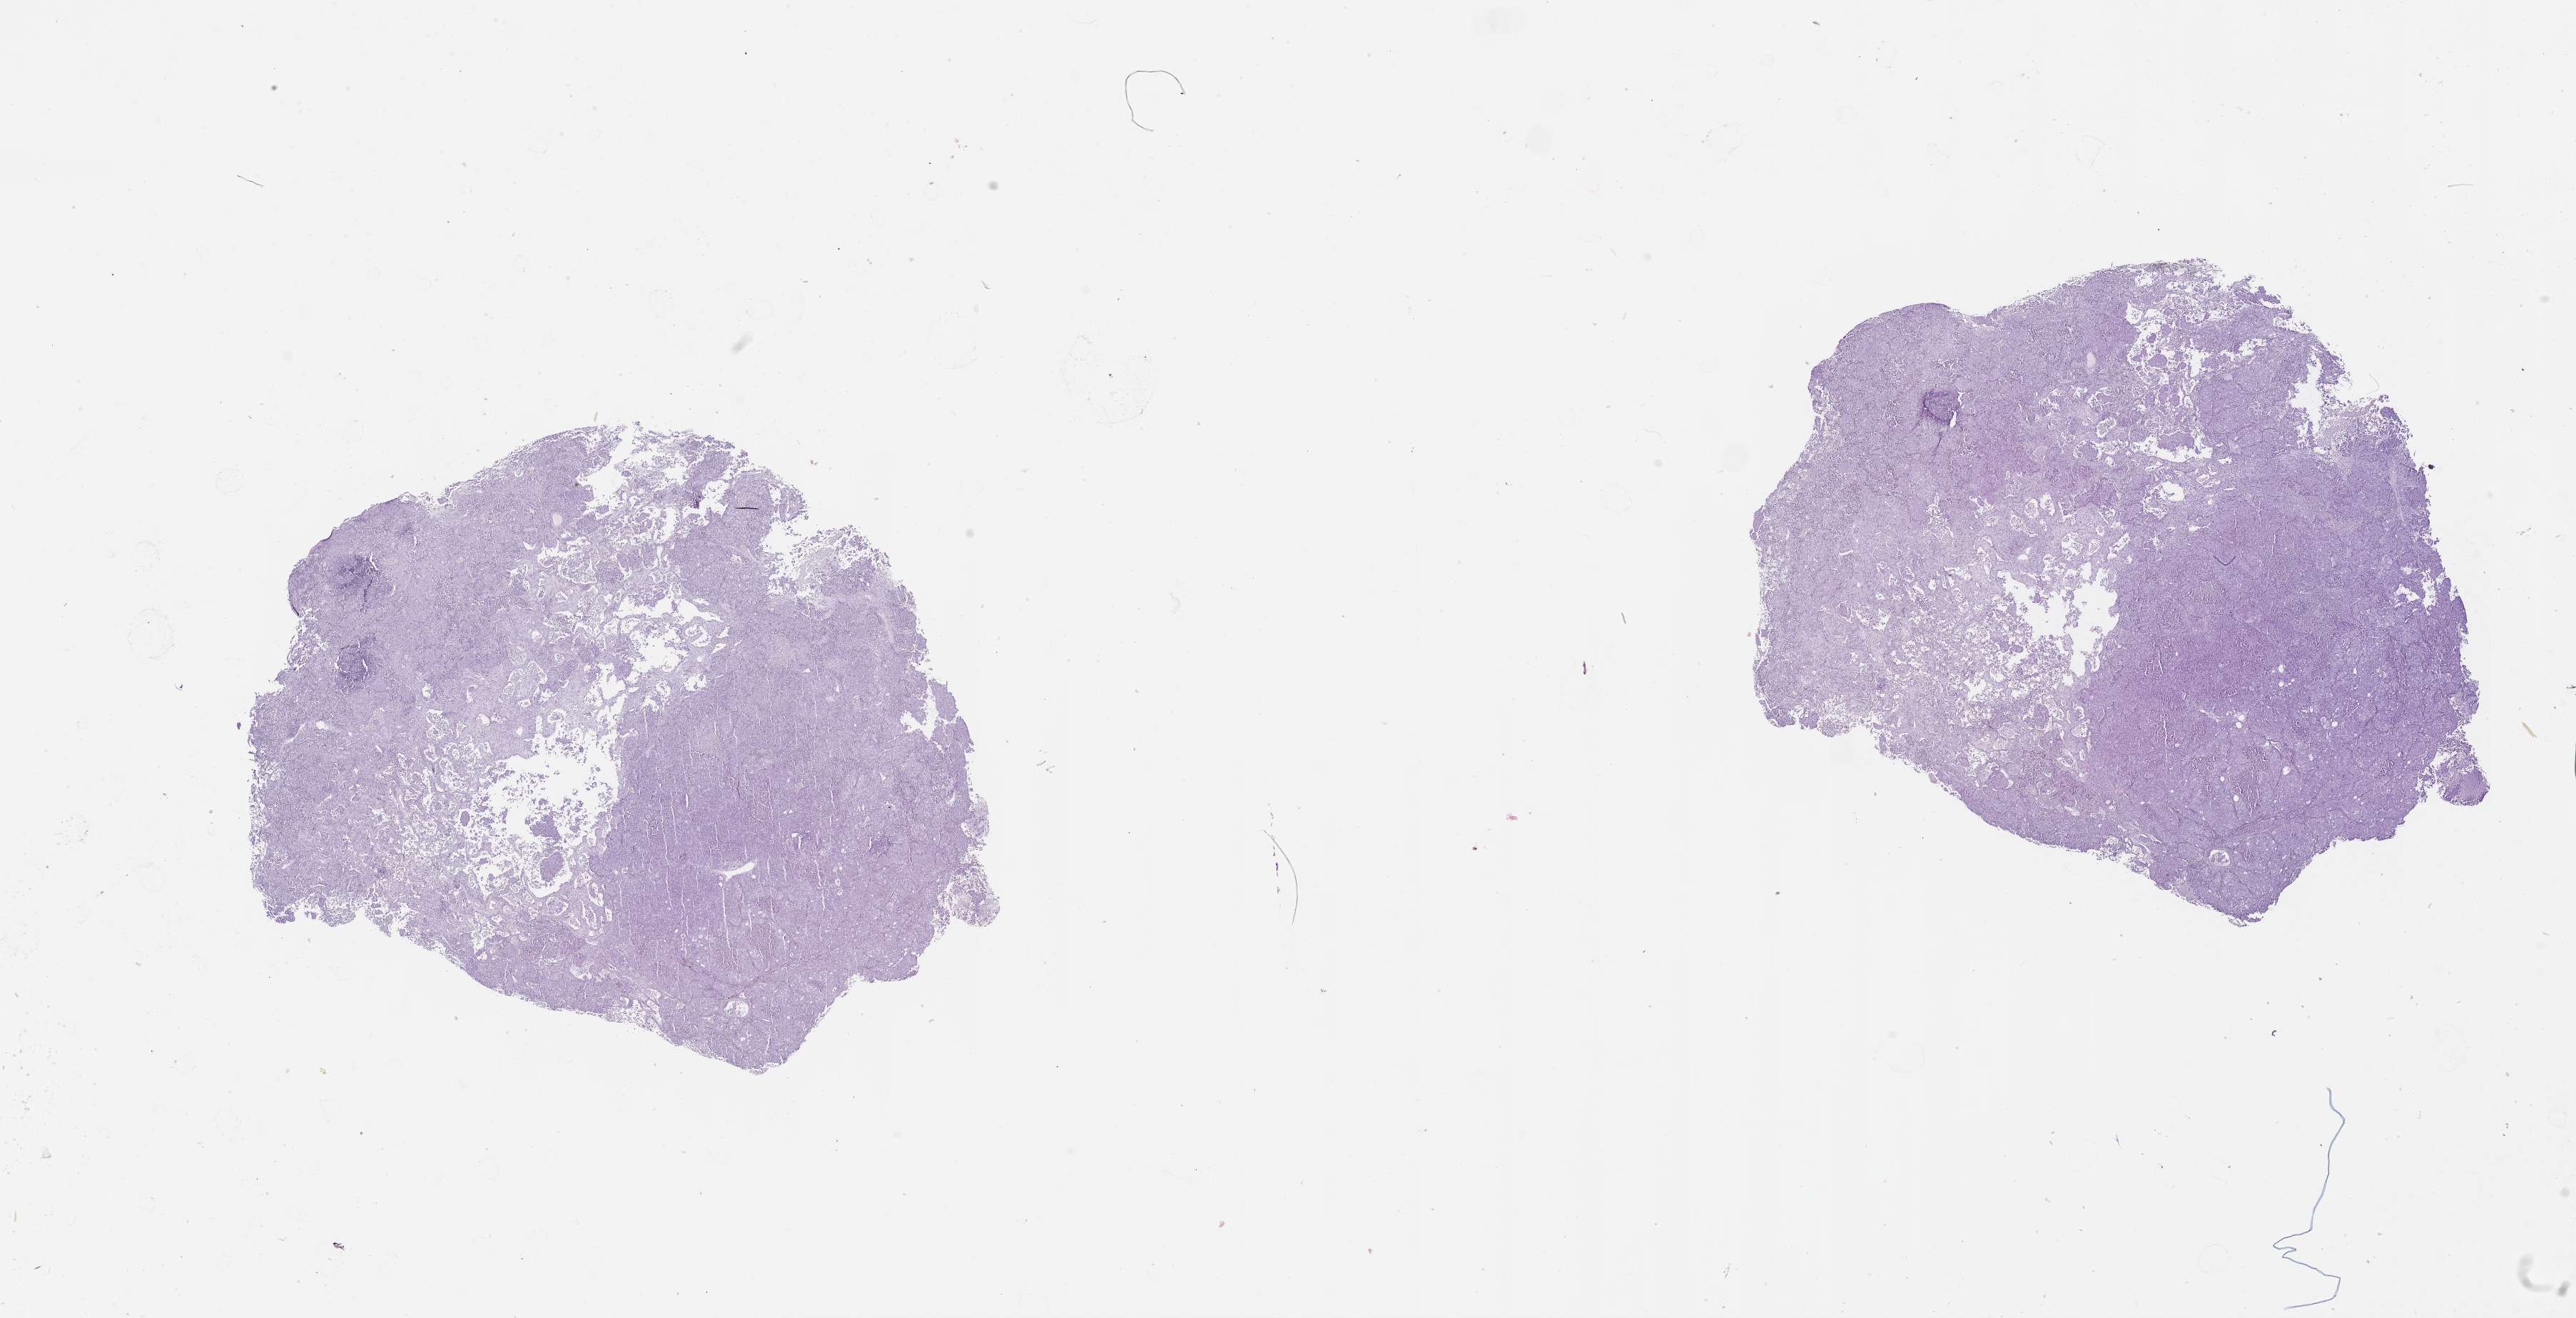
Digitized H&E tissue section (whole slide) — low-resolution overview of the scanned area, about 29.1 x 14.9 mm; lung, tissue type not recorded.
Patient diagnosis (cohort enrolment): lung adenocarcinoma (lung).